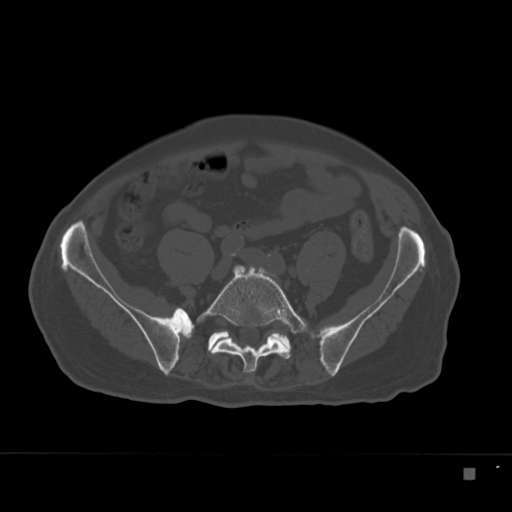
CT including the spine, one axial slice. Slice 20 of 332 in the series (ordered by position). Reconstruction kernel Br40s. 120 kVp. Bone window (W 1800 / L 400 HU). 512 × 512 image matrix, field of view 389 × 389 mm. Patient: male, 72 years. Case-level facts recorded for this patient, not image findings: primary cancer: skeletal.
Annotated regions visible in this slice (semi-automatically segmented with operator editing):
- L5 vertebra: bounding box (x1, y1, x2, y2) in pixels: (197, 265, 308, 373)